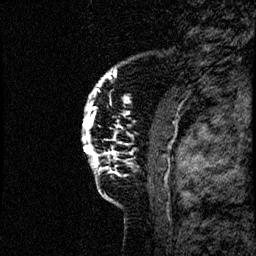
Breast MRI (dynamic contrast-enhanced), one sagittal slice. Position 12 of 60 along the scan axis. Dynamic contrast-enhanced study with each time point stored as its own series, time point 2 of 4 at this slice position (early post-contrast, ordered by acquisition time). 1.5 T. TE 4.2 ms, TR 17.6 ms. 2 mm slice thickness. 256 × 256 image matrix, field of view 200 × 200 mm. Female patient, age 40 years. From the clinical record (not read from this slice): setting: breast cancer imaged before/during neoadjuvant chemotherapy; receptor status: HER2-positive.
Structures marked on this image (semi-automatically segmented with operator editing):
- analysis volume of interest (the breast-tissue region the enhancement analysis was run in; not a lesion): bounding box <78,55,184,206> (left, top, right, bottom; pixels)
- tumour enhancement mask (voxels above the 100 % enhancement threshold inside the analysis volume of interest): <82,73,117,172>